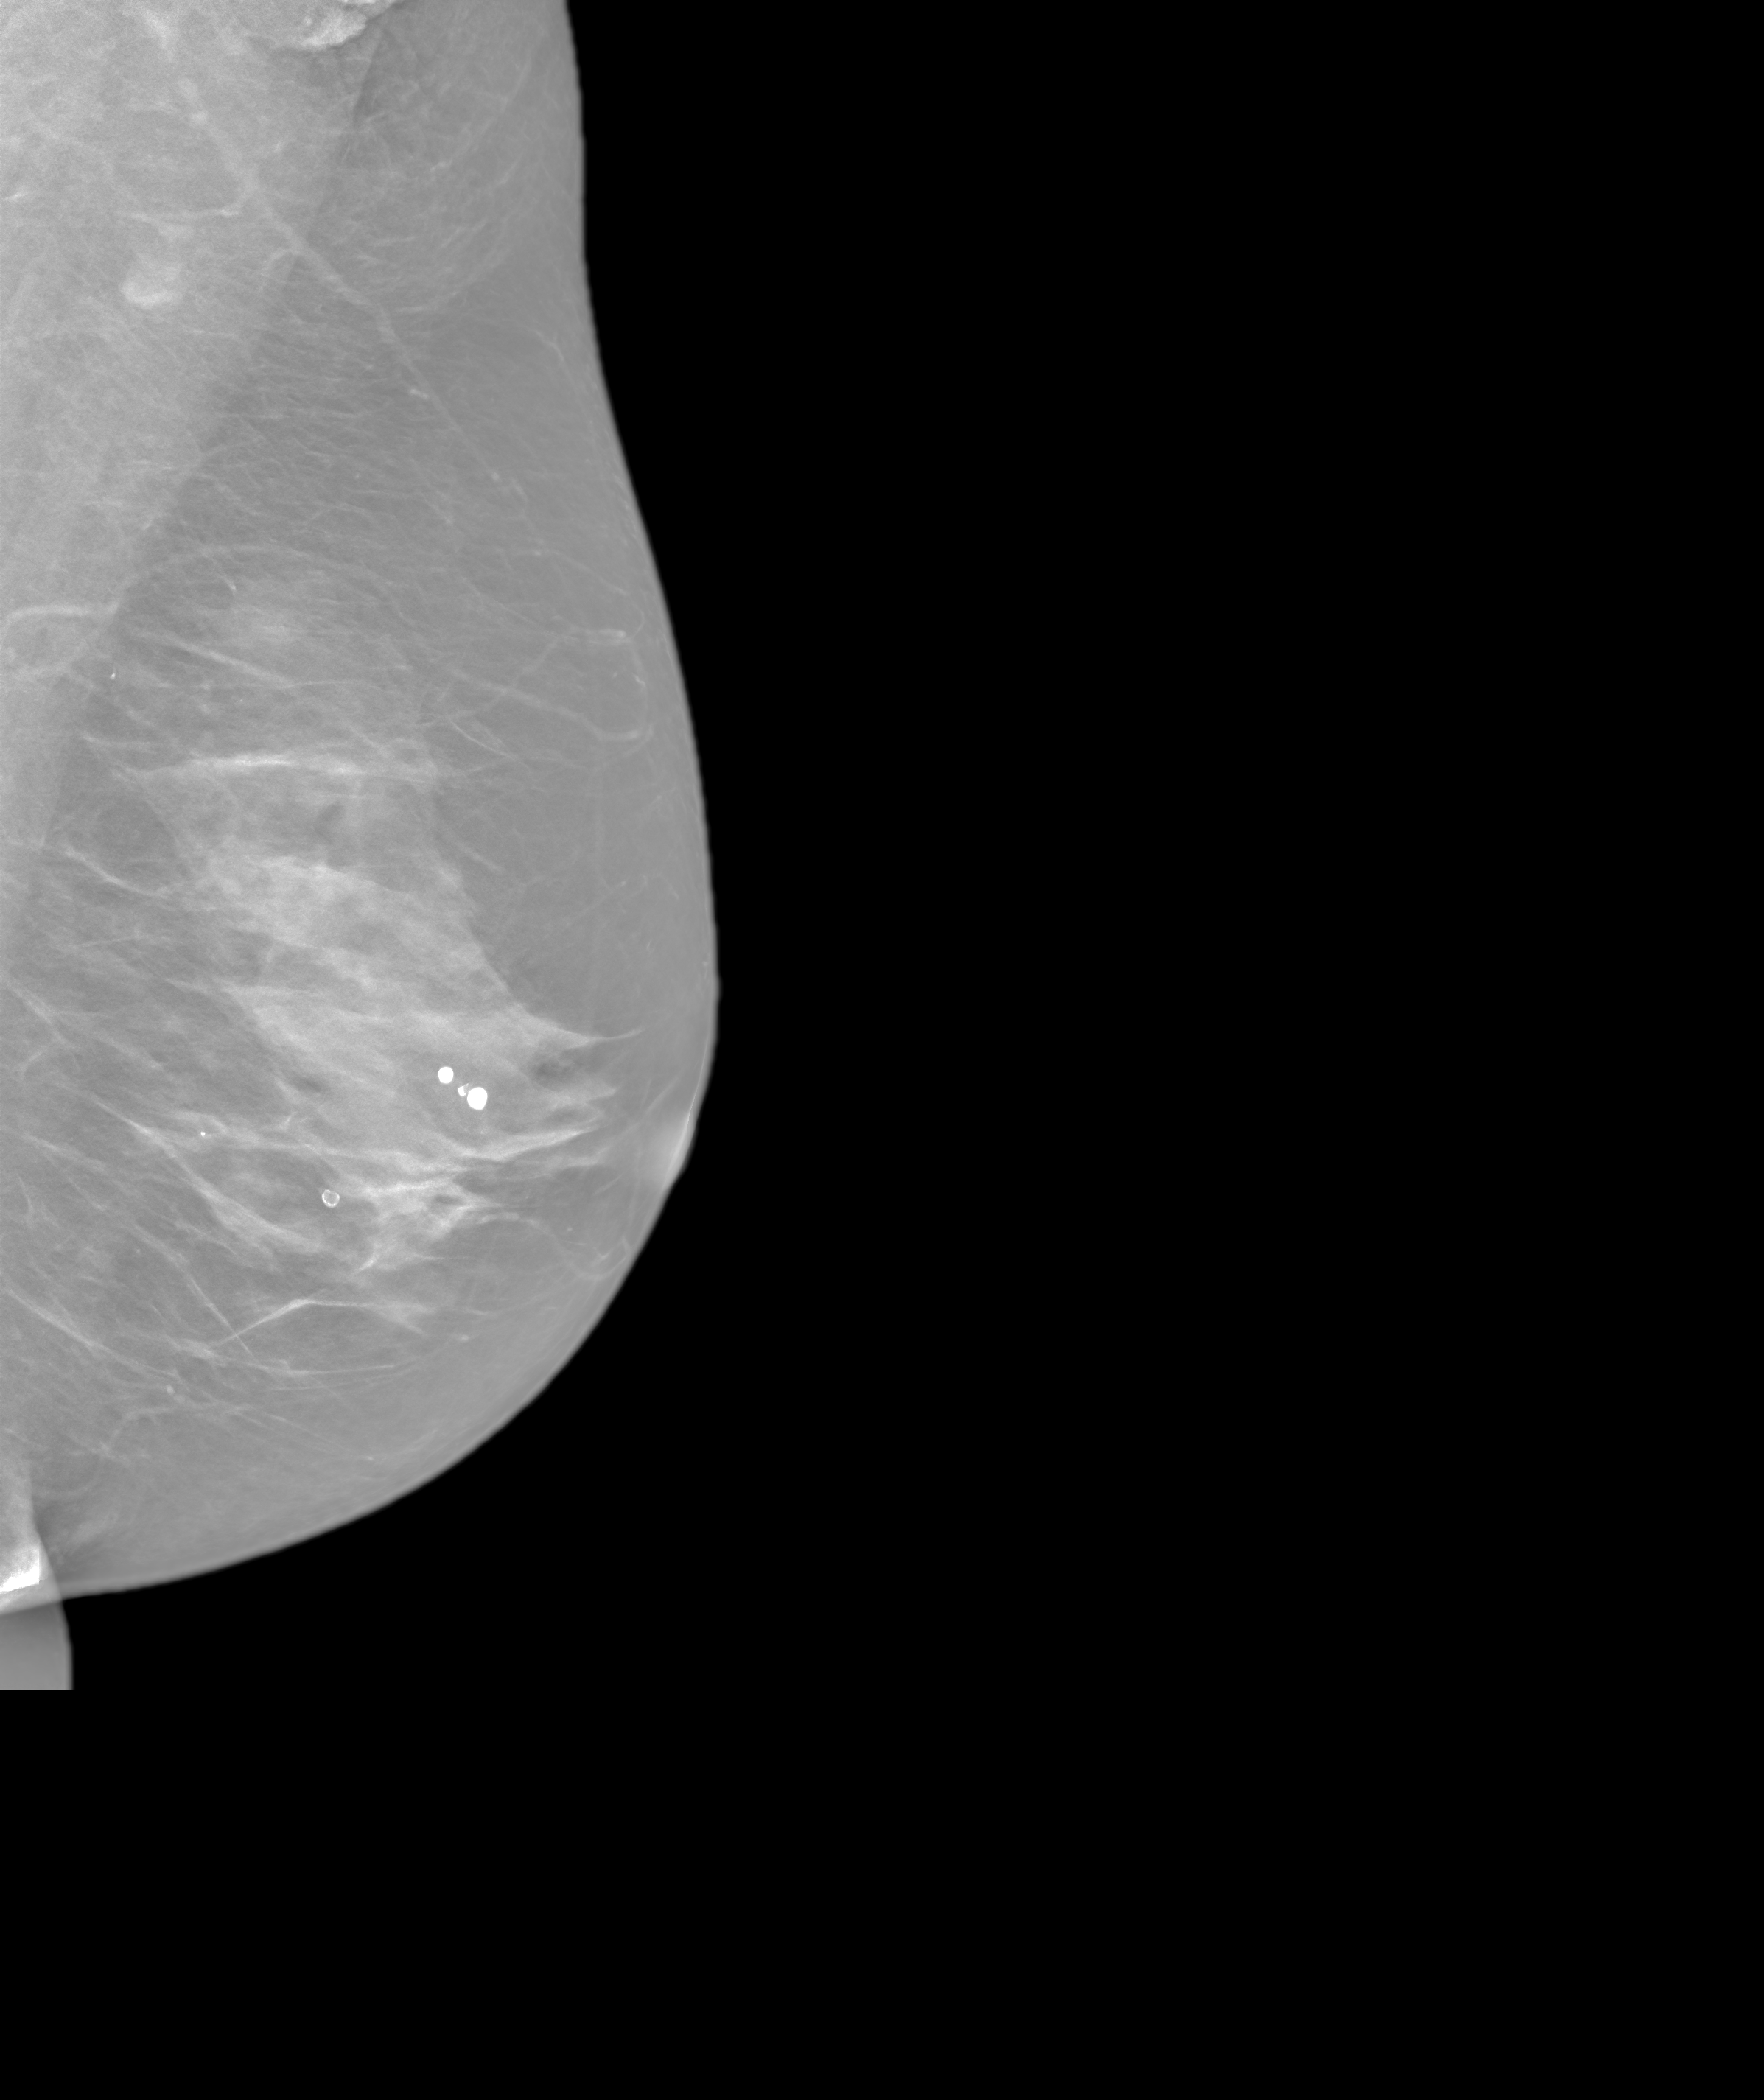
Screening examination, system: SenoIris_1SP1.2(425).
Image type: synthesized 2-D view from tomosynthesis. Breast: left. Projection: MLO view.